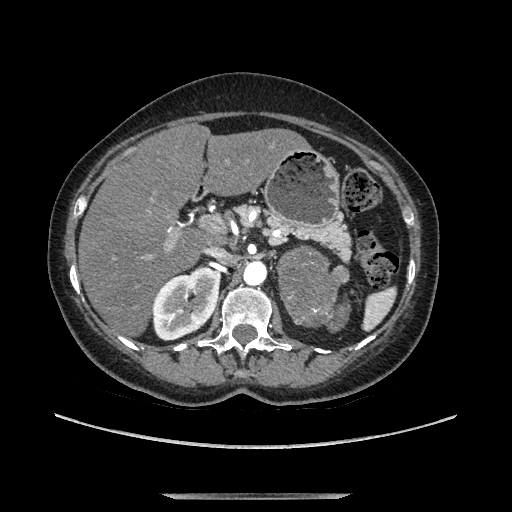
Contrast-enhanced abdominal CT, one axial slice; position 72 of 169 along the scan axis; soft-tissue window (W 400 / L 40 HU); 1.25 mm slice thickness; 512 × 512 image matrix, field of view 400 × 400 mm. Female patient. Case-level facts recorded for this patient, not image findings: diagnosis: adrenocortical carcinoma; tumour side: left adrenal; tumour size at pathology: 9 cm; Ki-67 index: 2 %; stage (as recorded): 3.
Annotated regions visible in this slice (semi-automatically segmented with operator editing):
- mass: box from (x=282, y=250) to (x=347, y=323) px